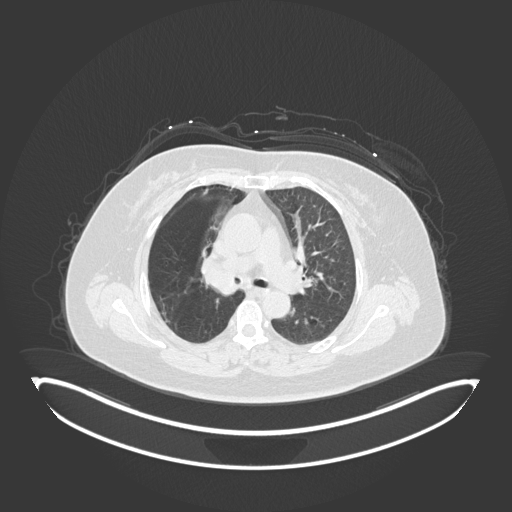
Chest CT, one axial slice; position 107 of 245 along the scan axis; reconstruction kernel B30f; 120 kVp; lung window (W 1500 / L -600 HU); 512 × 512 image matrix, field of view 500 × 500 mm. Patient: female, 60 years. Case-level facts recorded for this patient, not image findings: clinical TNM (as recorded): T1c N0 M0; histopathological grade: G1-G2.
Outlined on this slice (bounding box drawn by a radiologist):
- lung tumour (recorded histology: squamous cell carcinoma): bounding box <197,253,239,298> (left, top, right, bottom; pixels)